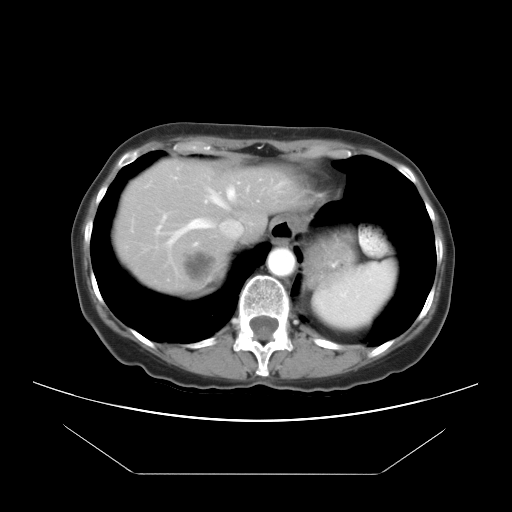
Contrast-enhanced abdominal CT, one axial slice. Reconstruction kernel STANDARD. 120 kVp. Intravenous contrast given. Soft-tissue window (W 400 / L 40 HU). 7.5 mm slice thickness. 512 × 512 image matrix, field of view 392 × 392 mm. Female patient, age 72 years. Case-level facts recorded for this patient, not image findings: diagnosis: colorectal cancer liver metastases, imaged before liver resection; multiple liver metastases: yes; largest metastasis: 4 cm; disease in both lobes: yes.
Outlined on this slice (outlined manually by an expert reader):
- hepatic veins: bounding box <167,188,235,246> (left, top, right, bottom; pixels)
- liver: <115,160,294,292>
- planned liver remnant (the part of the liver to remain after resection): <115,160,292,263>
- liver metastasis: <213,163,228,178>
- liver metastasis: <182,249,218,285>